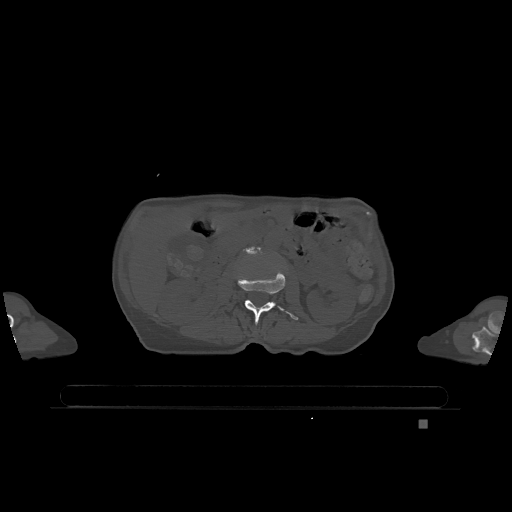
CT including the spine, one axial slice; position 407 of 1317 along the scan axis; bone window (W 1800 / L 400 HU); 0.5 mm slice thickness; 512 × 512 image matrix. Patient: female, 74 years. Case-level facts recorded for this patient, not image findings: primary cancer: lung.
Outlined on this slice (semi-automatically segmented with operator editing):
- L2 vertebra: box from (x=238, y=271) to (x=299, y=325) px
- L3 vertebra: (x=245, y=247)–(x=261, y=254)